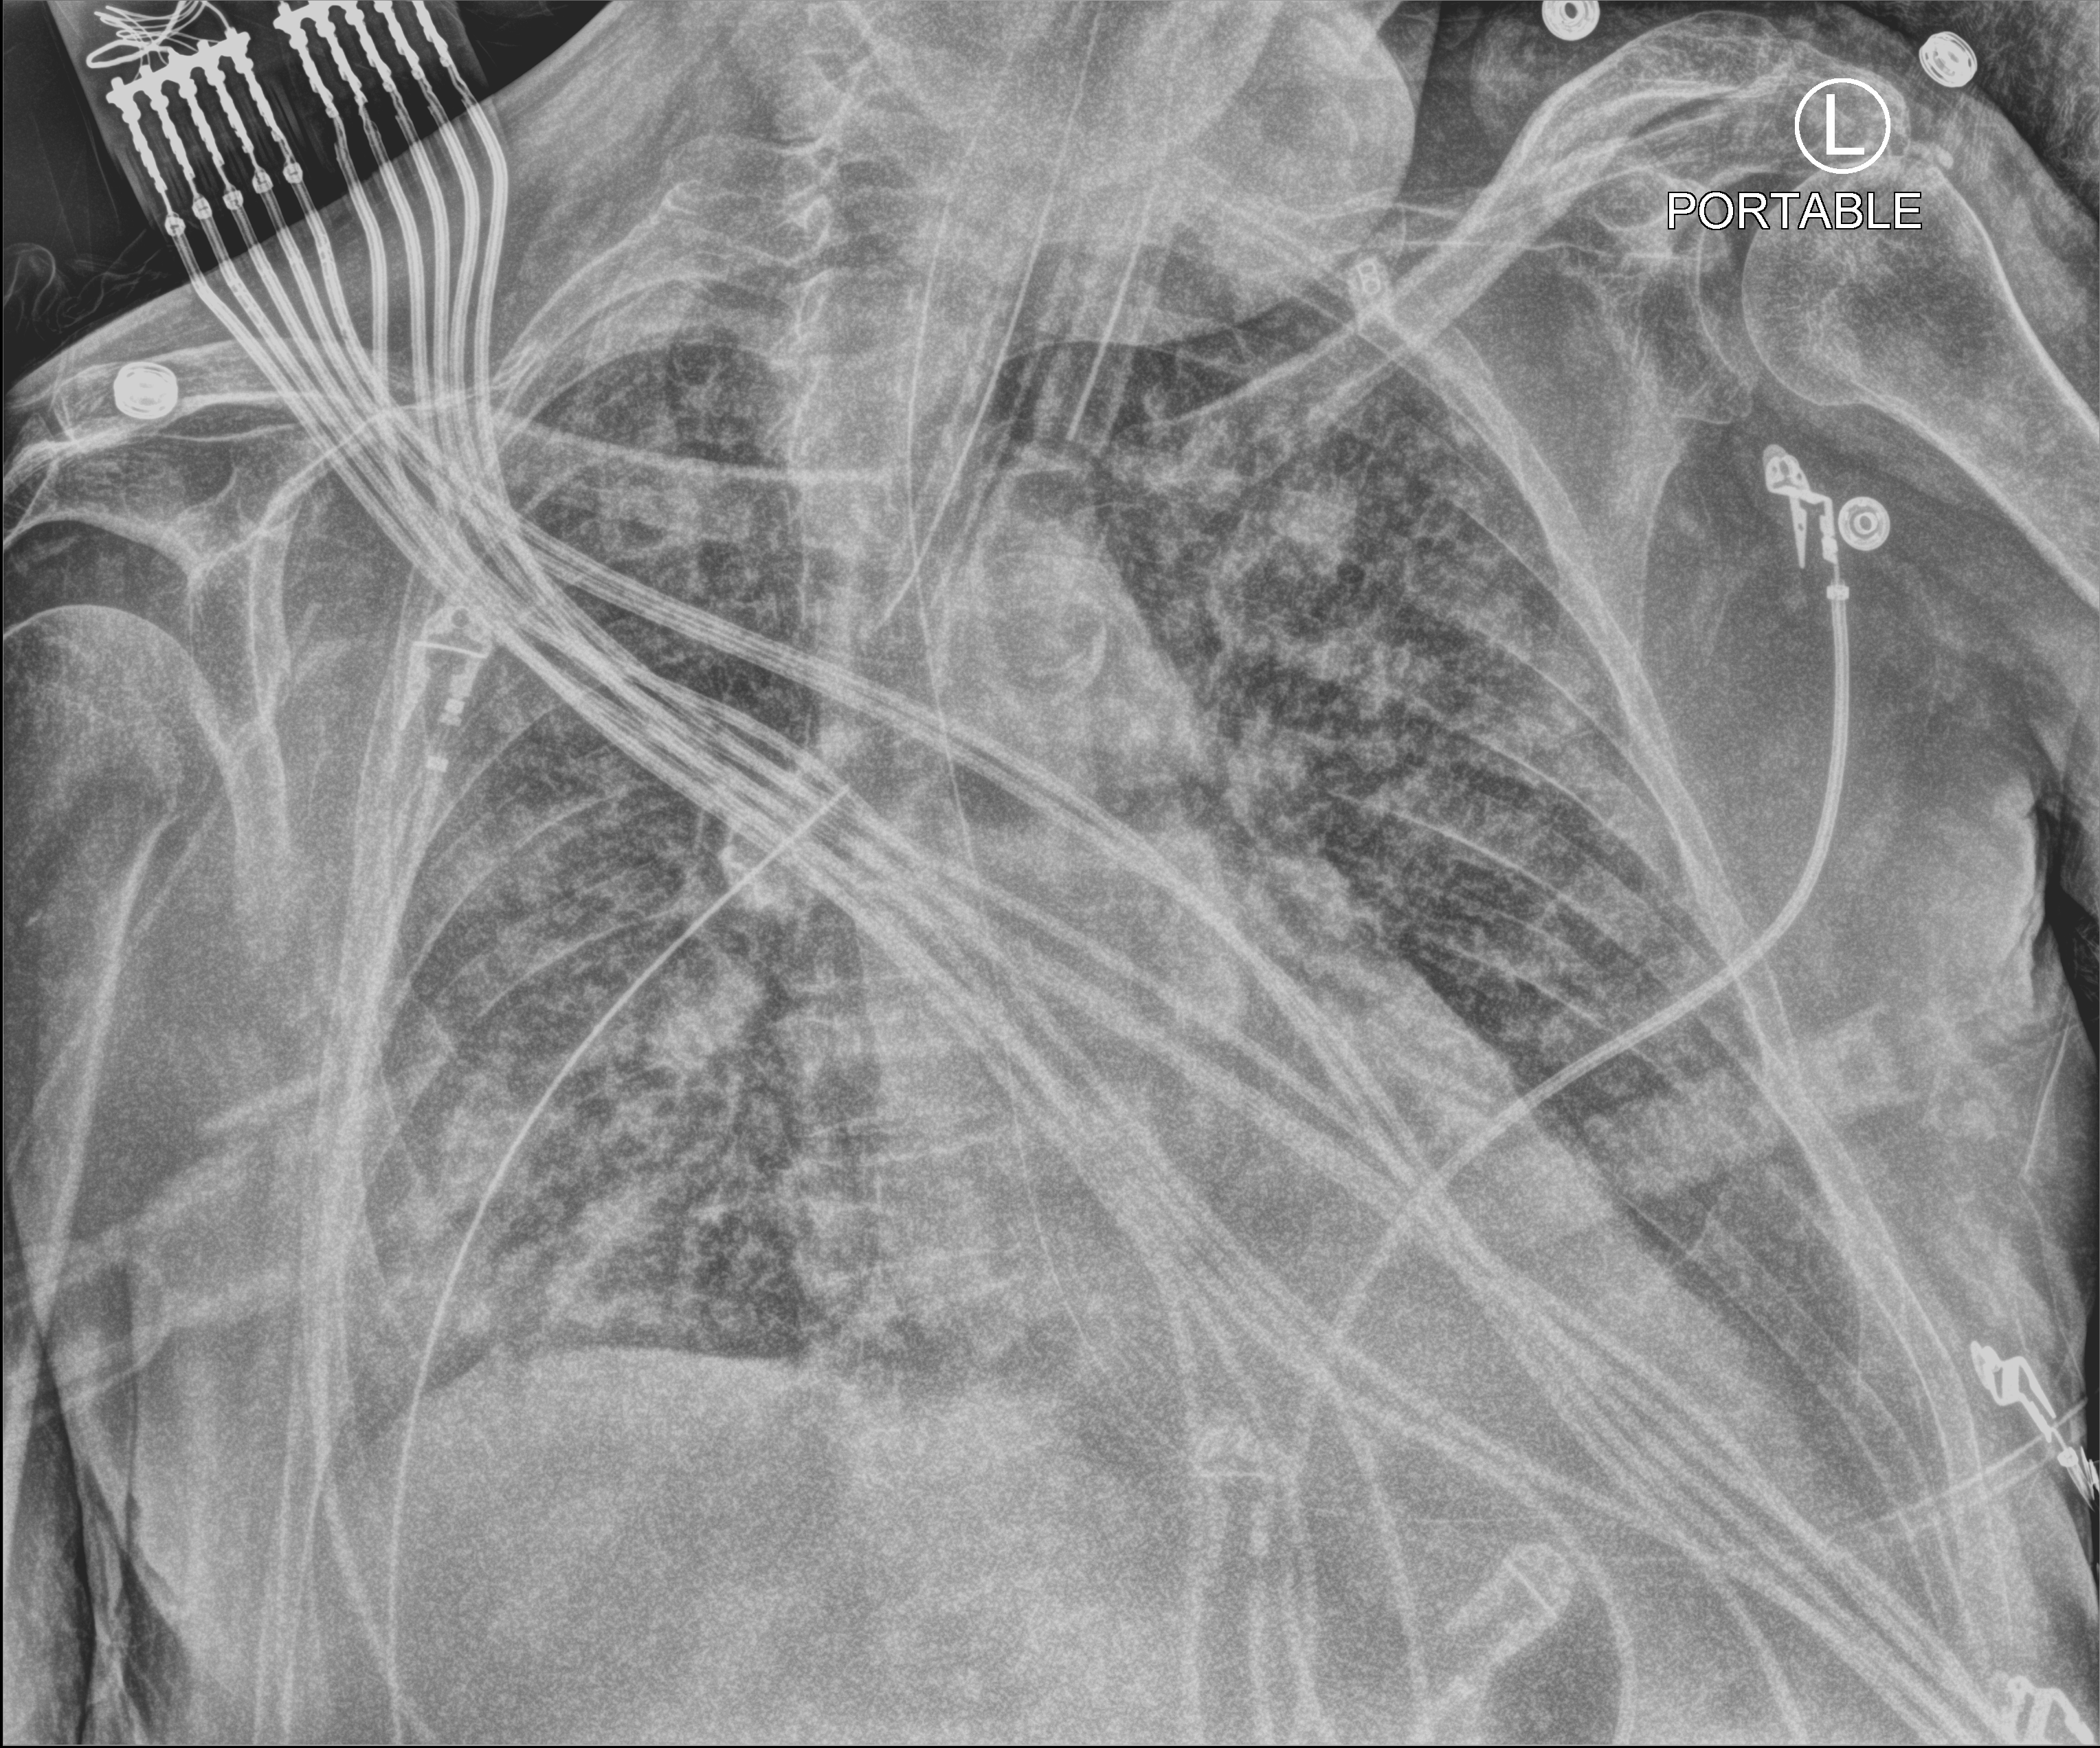
Chest X-ray (portable), anteroposterior (AP) projection. Male patient hospitalised with COVID-19, age 60–74 years.
From the hospital-stay record, not from the radiograph (when in the stay this image was taken is not recorded): admitted to intensive care during this hospital stay: yes.